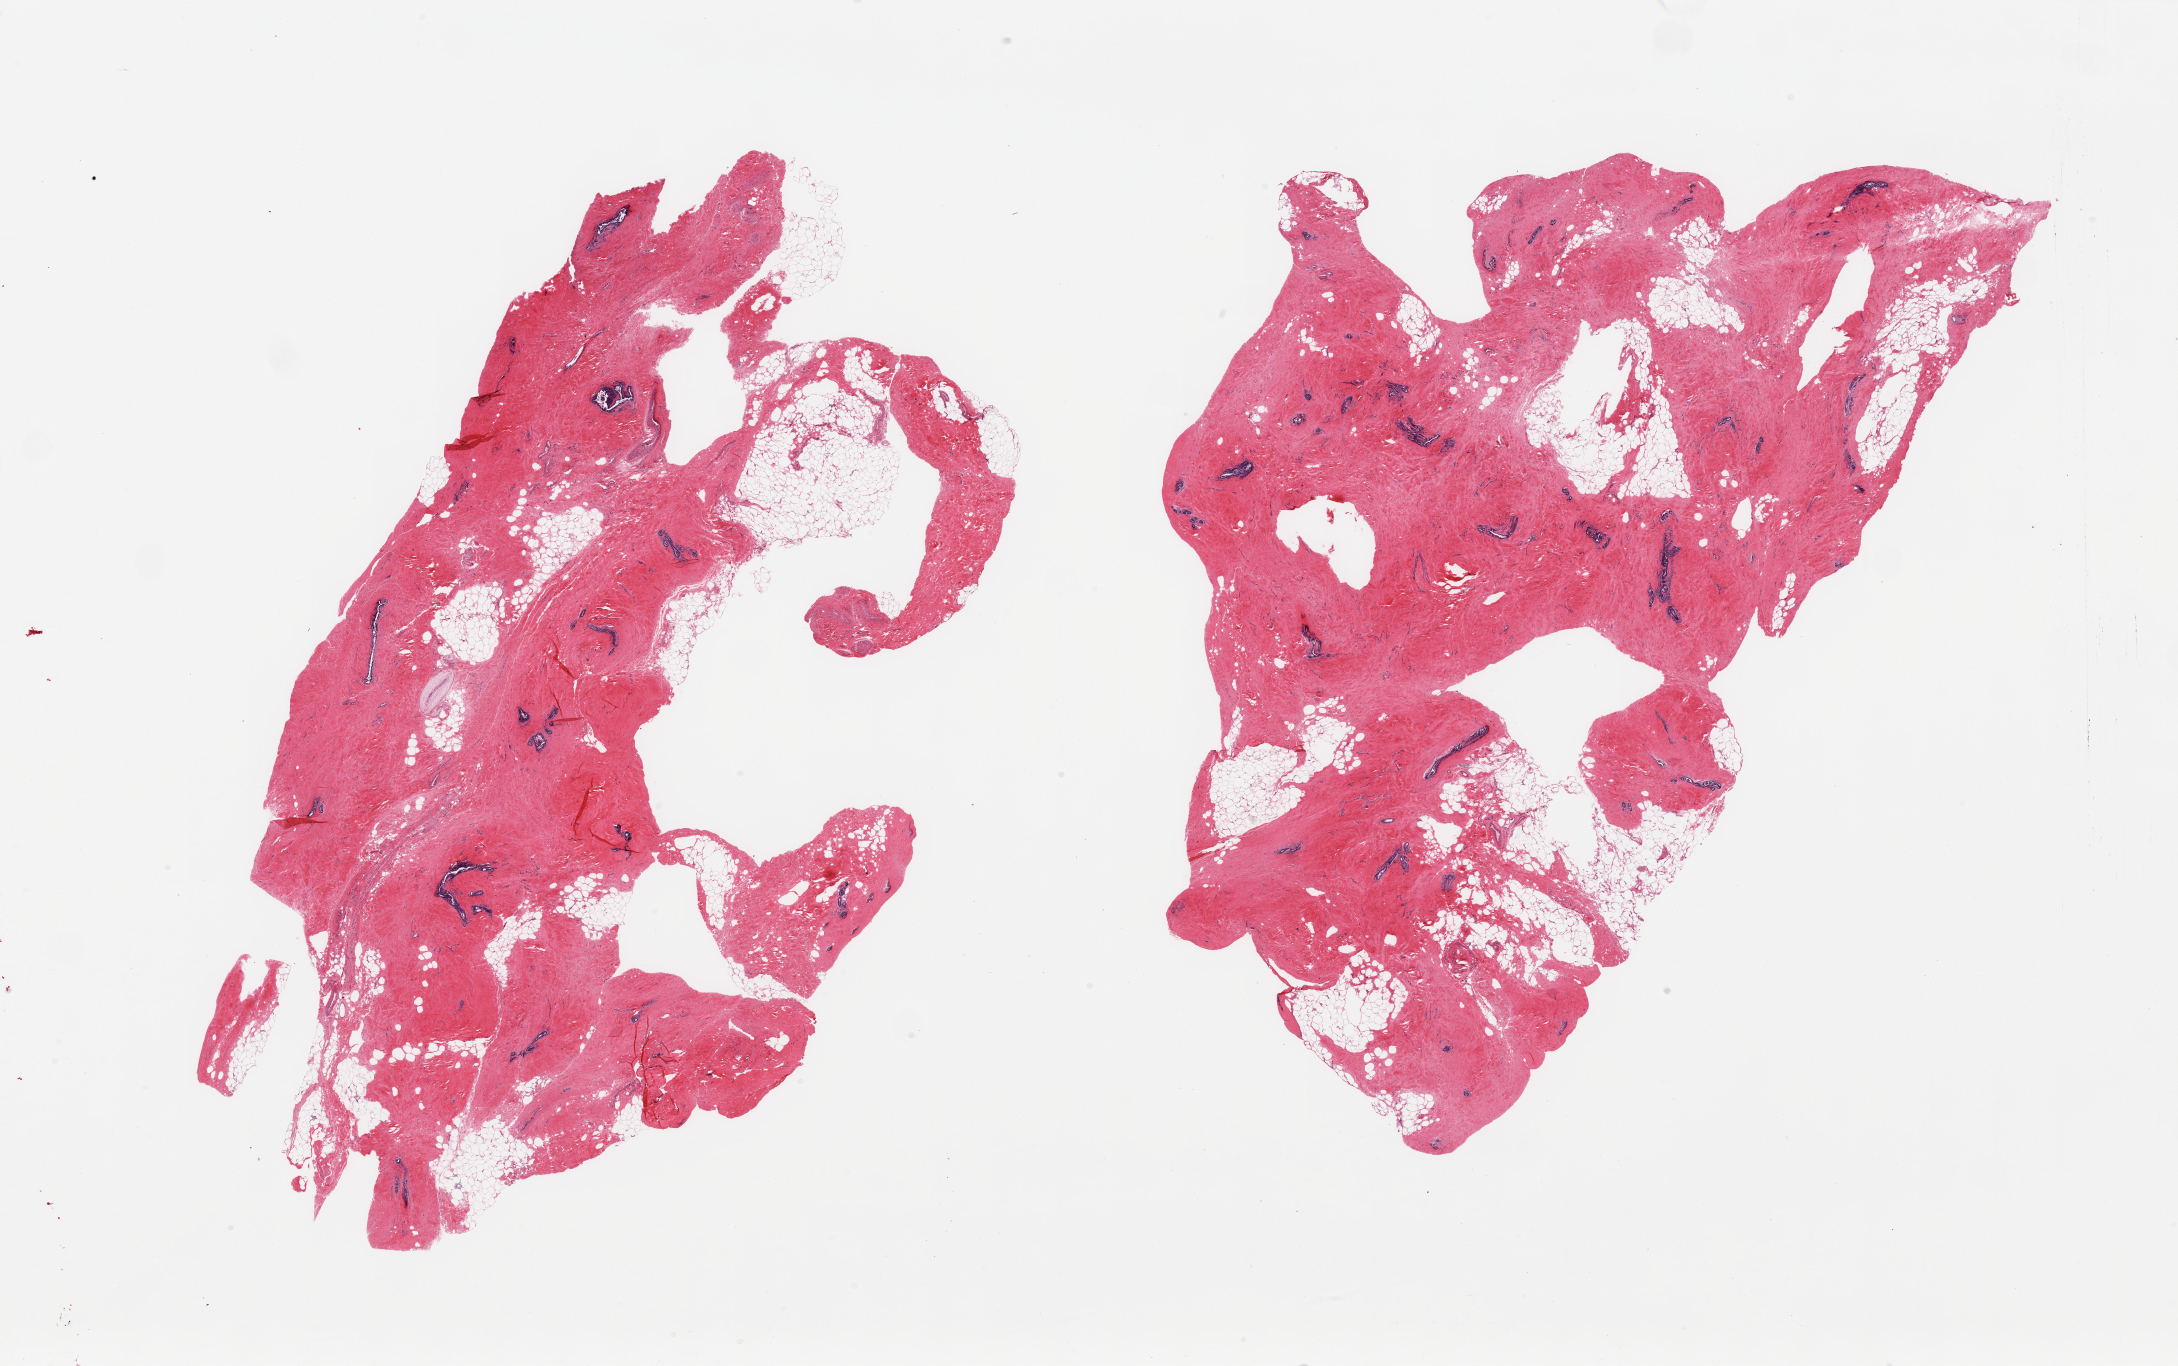
Whole-slide image, haematoxylin and eosin stain, a low-resolution overview of the entire scanned area, about 34.5 x 21.6 mm; PAXgene-fixed paraffin-embedded (PFPE) section; target tissue: breast; donor tissue sample. Male donor.
Pathologist's review note for this sample: 2 pieces, gynecomastoid stromal and ductal hyperplasia, pronounced.